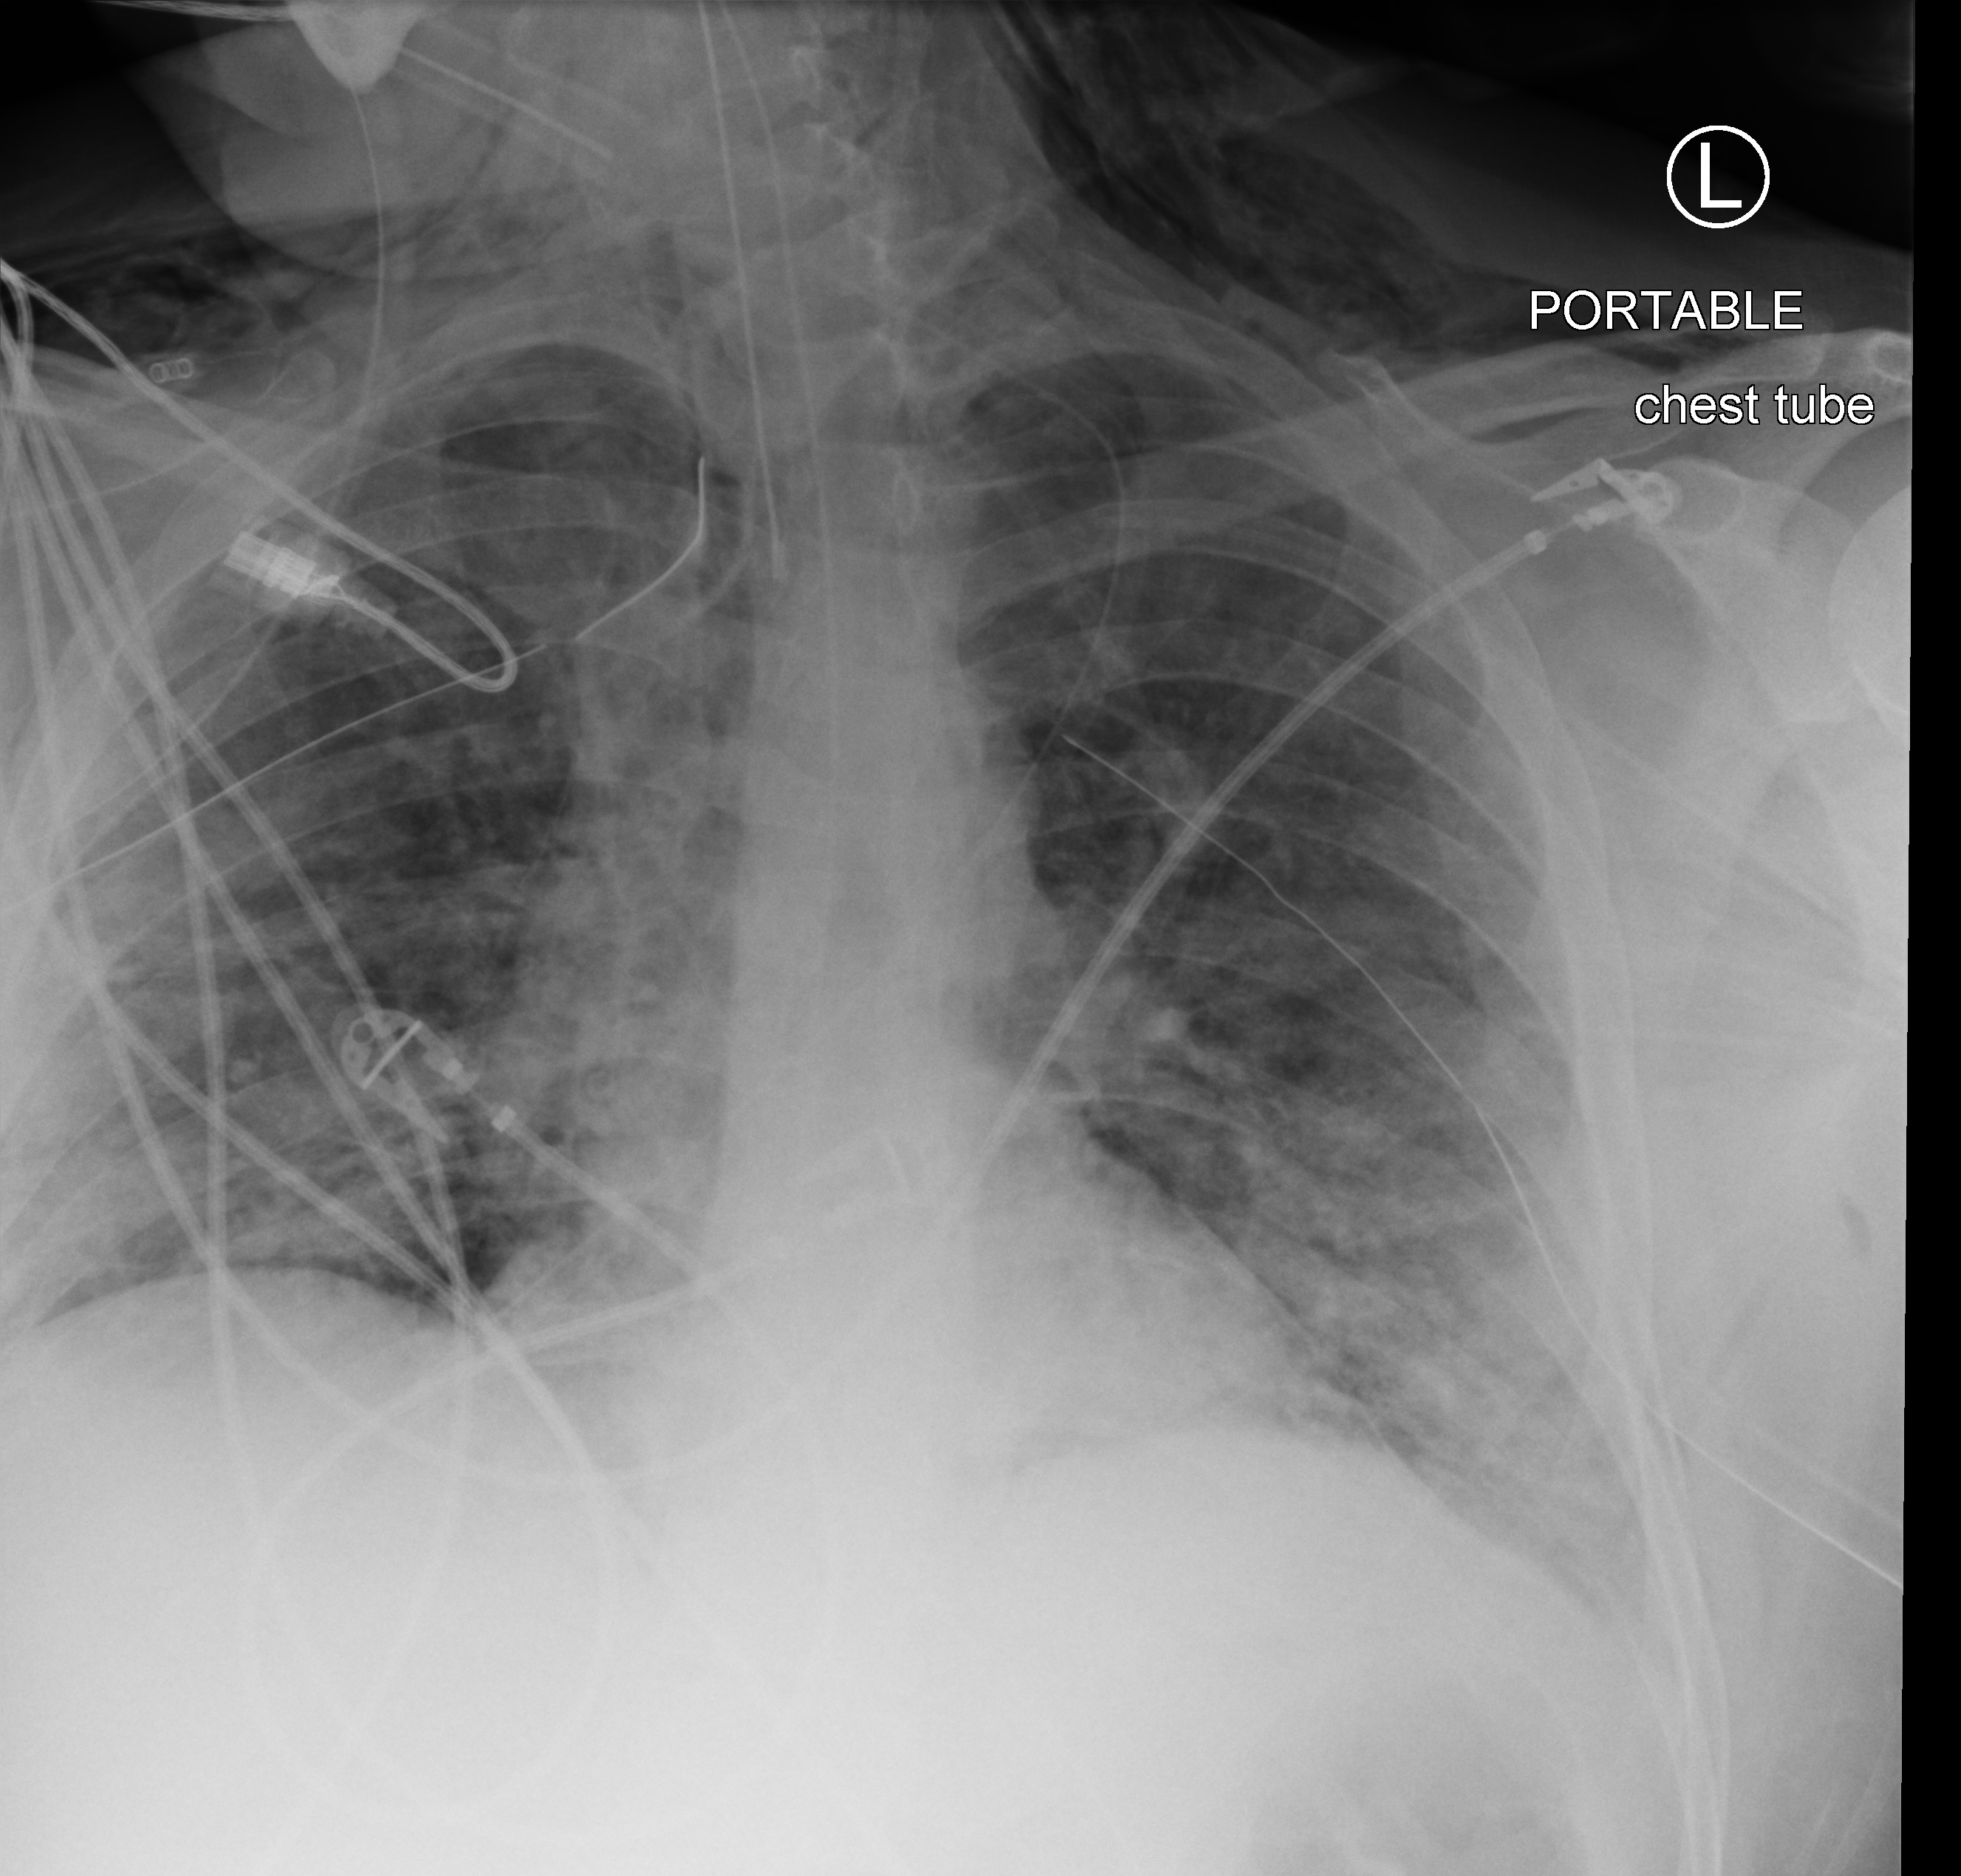
Chest X-ray (portable); anteroposterior (AP) projection. Patient hospitalised with COVID-19; male, aged 18–59 years.
Admission-level facts for this patient (not findings on this image; timing relative to this image not recorded):
- length of hospital stay: 63 days